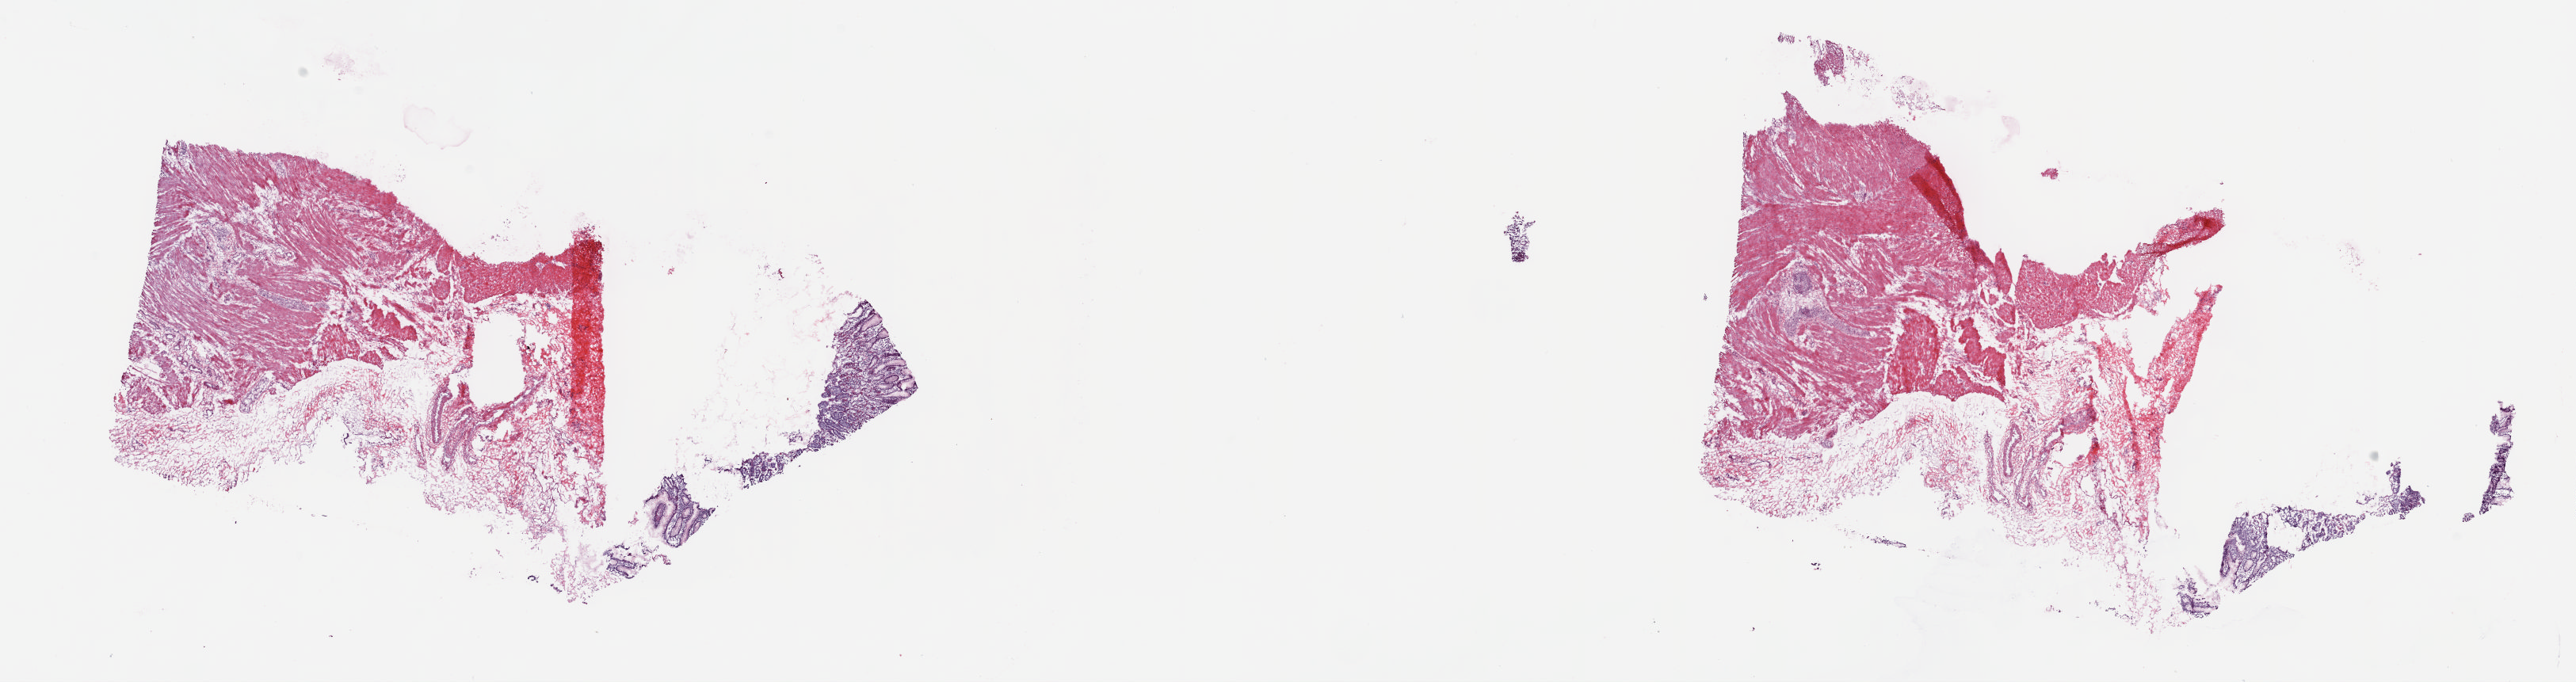
Hematoxylin and eosin (H&E) stained whole-slide image, shown as a low-resolution overview of the whole scanned area (about 25.8 x 6.8 mm). Frozen section. Stomach, solid tissue normal (non-tumour tissue) sample. Female patient; age at initial diagnosis 61 years. Composition of this section per pathologist review: tumour cells 0%, tumour nuclei 0%, normal cells 50%, stromal cells 50%, necrosis 0%. Infiltration values recorded for this section: lymphocyte infiltration 40%, monocyte infiltration 20%, neutrophil infiltration 20%.
This section: solid tissue normal sample (biorepository sample class). Patient diagnosis: Signet ring cell carcinoma (gastric antrum).